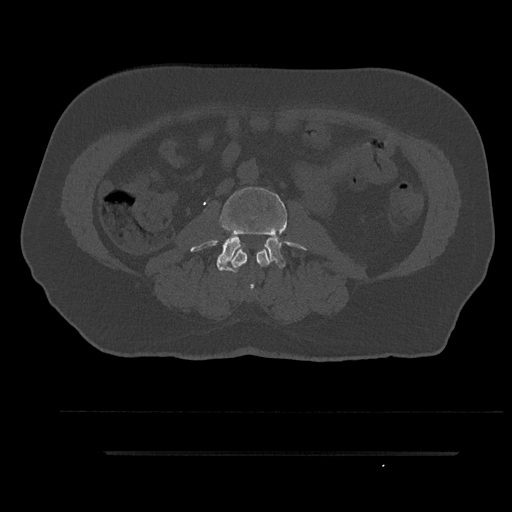
CT including the spine, one axial slice; slice 65 of 797 in the series (ordered by position); bone window (W 1800 / L 400 HU); 0.5 mm slice thickness; 512 × 512 image matrix, field of view 432 × 432 mm. Patient: male, 63 years. From the clinical record (not read from this slice): primary cancer: renal; vertebrae with lytic lesions (as recorded): T8.
Outlined on this slice (semi-automatically segmented with operator editing):
- L2 vertebra: bounding box (x1, y1, x2, y2) in pixels: (232, 249, 269, 291)
- L3 vertebra: (190, 185, 305, 272)